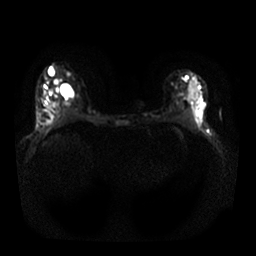
Breast MRI, one axial slice. Position 14 of 25 along the scan axis. Diffusion-weighted series; image 2 of 4 stored at this slice position (different b-values; order by instance number). 1.5 T. 4 mm slice thickness. 256 × 256 image matrix. Female patient.
Annotated regions visible in this slice (manually delineated by an expert):
- tumour on diffusion-weighted imaging: box from (x=192, y=87) to (x=203, y=107) px